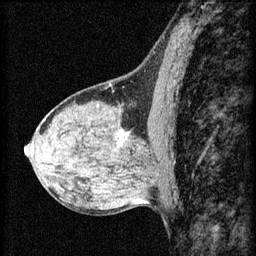
Breast MRI (dynamic contrast-enhanced), one sagittal slice. Slice 31 of 60 in the series (ordered by position). 3 images stored at this slice position (order not interpretable as contrast timing). 1.5 T. TE 4.2 ms, TR 8.2 ms. 2 mm slice thickness. 256 × 256 image matrix, field of view 180 × 180 mm. Female patient, age 40 years.
Annotated regions visible in this slice (semi-automatically segmented with operator editing):
- analysis volume of interest (the breast-tissue region the enhancement analysis was run in; not a lesion): bounding box <104,116,143,165> (left, top, right, bottom; pixels)
- tumour enhancement mask (voxels above the 70 % enhancement threshold inside the analysis volume of interest): <118,144,121,147>